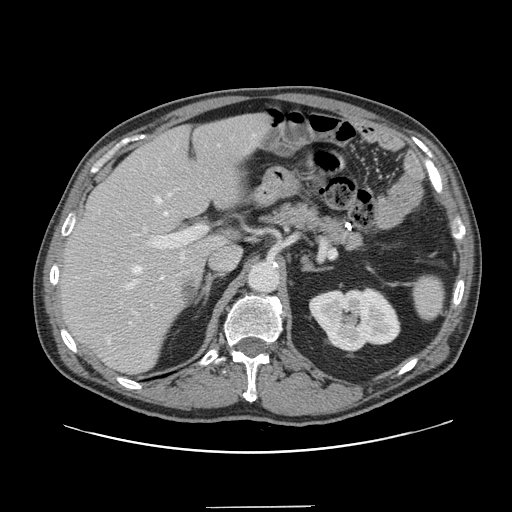
Contrast-enhanced abdominal CT, one axial slice. Position 92 of 139 along the scan axis. Intravenous contrast given. Soft-tissue window (W 400 / L 40 HU). 512 × 512 image matrix, field of view 397 × 397 mm. Male patient, age 64 years. From the clinical record (not read from this slice): diagnosis: colorectal cancer liver metastases, imaged before liver resection.
Structures marked on this image (manually delineated by an expert):
- hepatic veins: box from (x=126, y=134) to (x=255, y=324) px
- liver: (x=62, y=115)–(x=269, y=373)
- planned liver remnant (the part of the liver to remain after resection): (x=62, y=115)–(x=269, y=373)
- portal vein (with intrahepatic branches): (x=121, y=225)–(x=208, y=315)
- liver metastasis: (x=184, y=284)–(x=194, y=299)